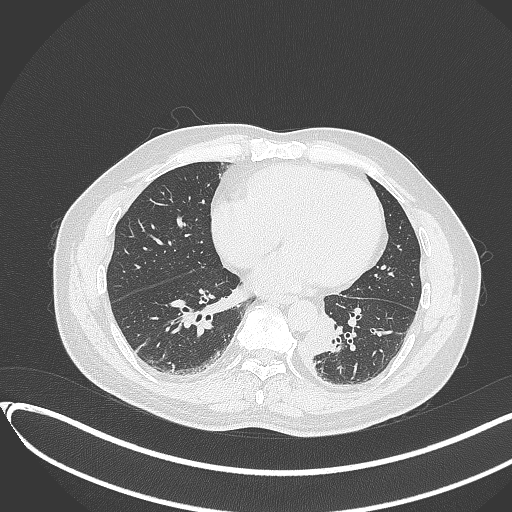
Chest CT, one axial slice. Slice 123 of 417 in the series (ordered by position). 120 kVp. Lung window (W 1500 / L -600 HU). 512 × 512 image matrix, field of view 400 × 400 mm. Patient: male, 54 years. Case-level facts recorded for this patient, not image findings: clinical TNM (as recorded): T3 N0 M0.
Outlined on this slice (bounding box drawn by a radiologist):
- lung tumour (recorded histology: squamous cell carcinoma): bounding box [x1, y1, x2, y2] px = [295, 303, 343, 361]